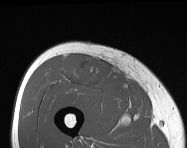
MRI of an extremity soft-tissue mass, one axial slice; slice 63 of 114 in the series (ordered by position); MR volume resampled by the dataset authors to the PET/CT grid (not the native acquisition matrix); 187 × 148 image matrix, field of view 183 × 145 mm. Male patient. Case-level facts recorded for this patient, not image findings: histological type: pleiomorphic leiomyosarcoma; grade: intermediate; site of the primary tumour: right thigh.
Annotated regions visible in this slice (expert contour drawn on MRI and transferred to this co-registered scan by the dataset authors):
- gross tumour volume including surrounding oedema: box from (x=63, y=54) to (x=110, y=85) px